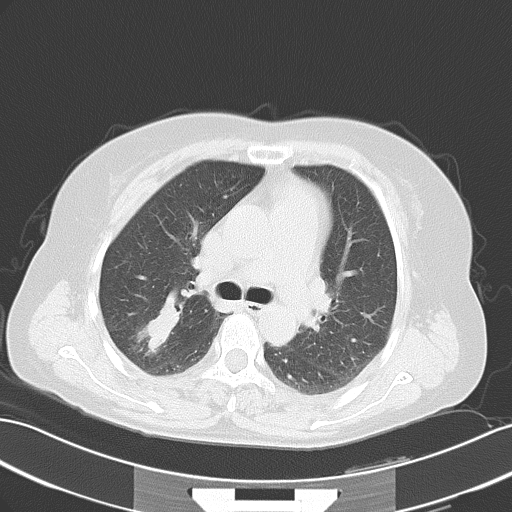
Chest CT, one axial slice. Slice 32 of 49 in the series (ordered by position). Lung window (W 1500 / L -600 HU). 512 × 512 image matrix, field of view 353 × 353 mm. Female patient, age 52 years. Case-level facts recorded for this patient, not image findings: clinical TNM (as recorded): T1c N3 M1a.
Structures marked on this image (bounding box drawn by a radiologist):
- lung tumour (recorded histology: adenocarcinoma): bounding box (x1, y1, x2, y2) in pixels: (133, 284, 190, 360)